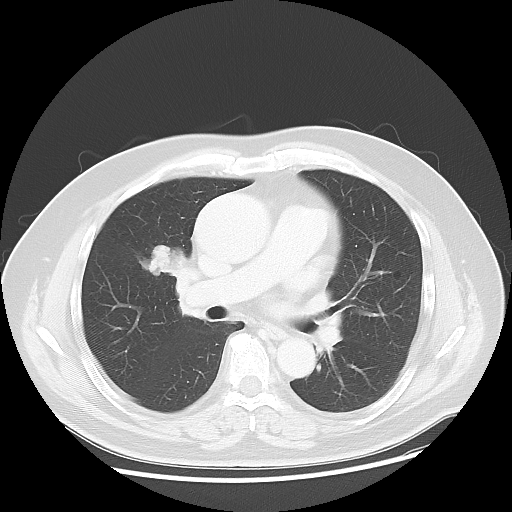
Chest CT, one axial slice. Position 24 of 48 along the scan axis. Lung window (W 1500 / L -600 HU). 5 mm slice thickness. 512 × 512 image matrix, field of view 392 × 392 mm. Patient: male, 60 years. Case-level facts recorded for this patient, not image findings: clinical TNM (as recorded): T2 N3 M0; histopathological grade: G2-3.
Annotated regions visible in this slice (rectangle marked by the reading radiologist):
- lung tumour (recorded histology: adenocarcinoma): bounding box [x1, y1, x2, y2] px = [133, 229, 187, 294]